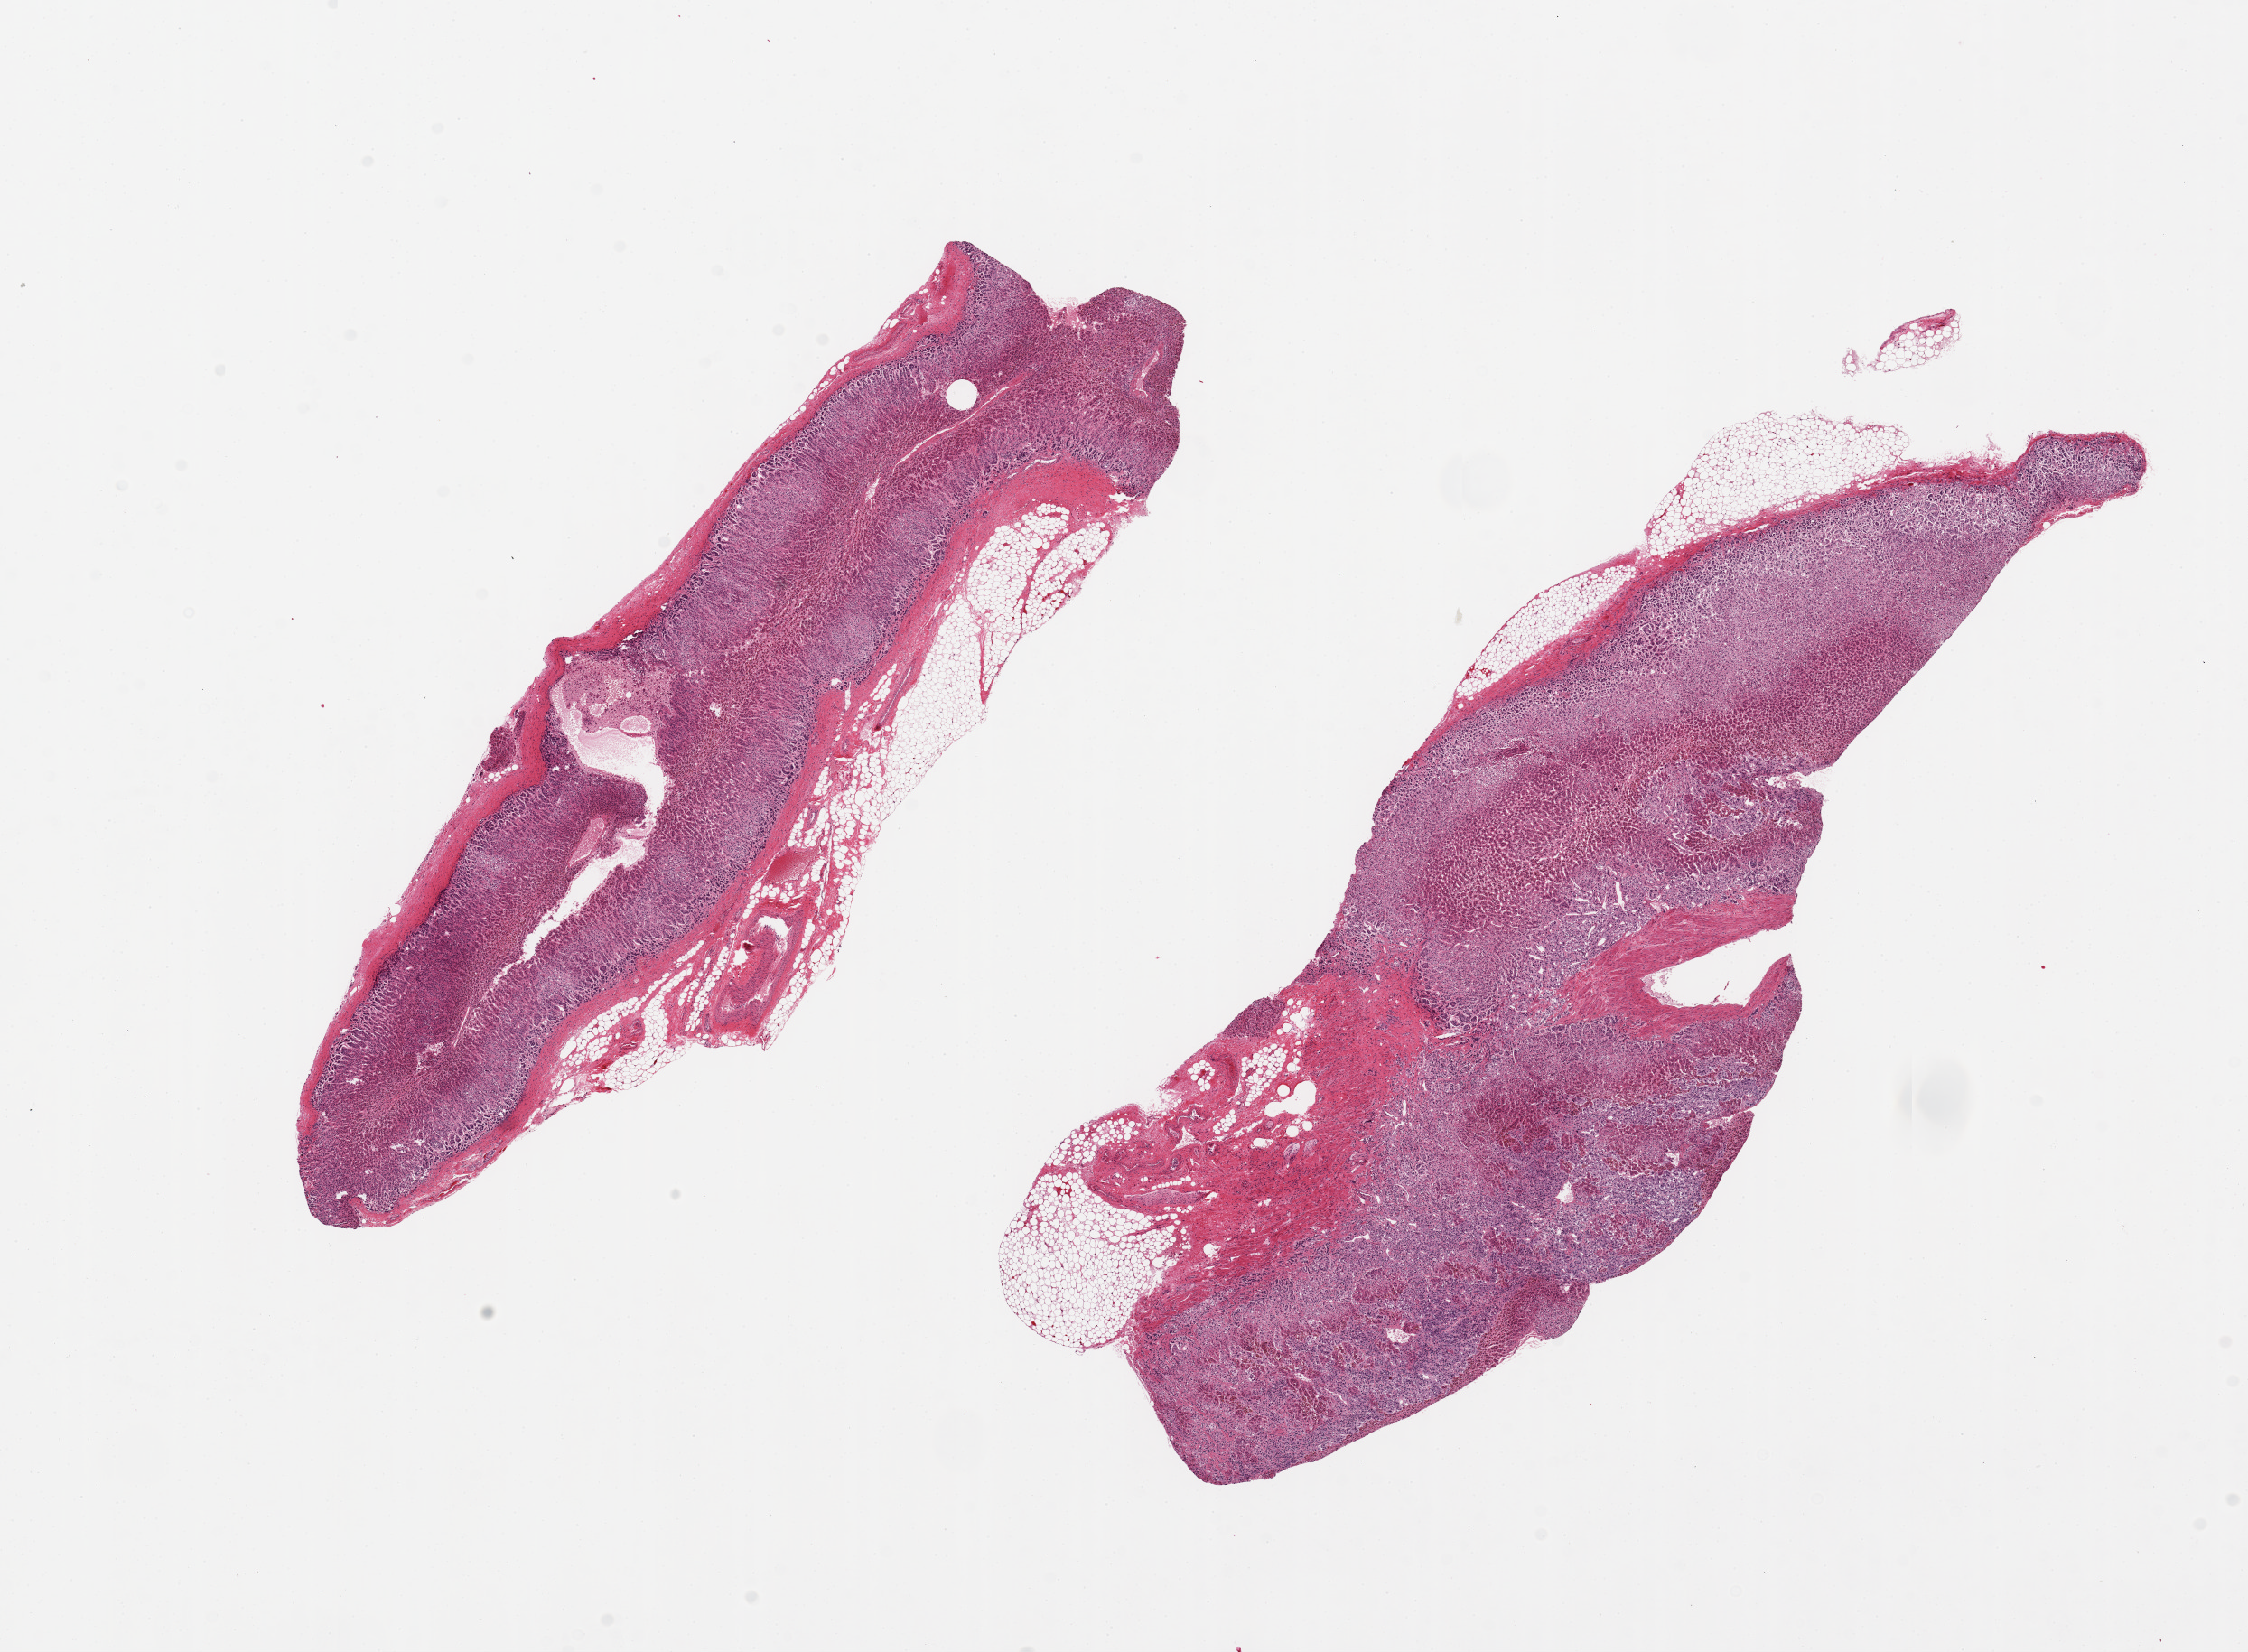
Hematoxylin and eosin (H&E) whole-slide image, low-resolution overview of the scanned area, about 19.7 x 14.5 mm (slide scanned at 20x); PAXgene-fixed paraffin-embedded (PFPE) section; target tissue: adrenal gland; donor tissue sample. Donor sex: male.
- reviewer comment on this tissue sample: 2 pieces, 11x4 & 12x5mm; all cortex, discontinuous rim of adherent fat on both, up to ~0.5-1mm thick